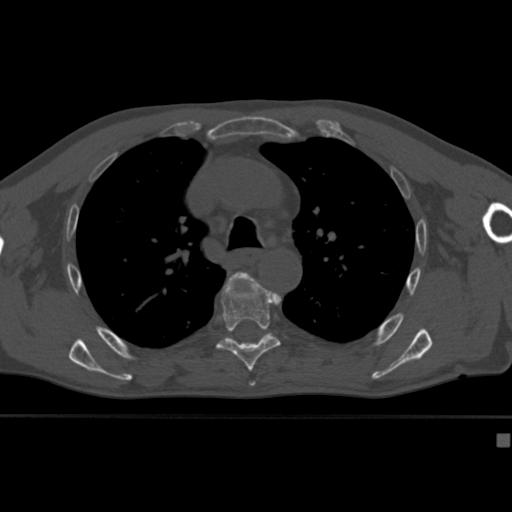
CT including the spine, one axial slice. Slice 295 of 430 in the series (ordered by position). Reconstruction kernel Br40s. Bone window (W 1800 / L 400 HU). 1.5 mm slice thickness. 512 × 512 image matrix. Patient: male, 64 years. From the clinical record (not read from this slice): primary cancer: uterus; vertebrae with lytic lesions (as recorded): T1, T4, T5, T7, L5.
Annotated regions visible in this slice (semi-automatically segmented with operator editing):
- T5 vertebra: bounding box [x1, y1, x2, y2] px = [230, 271, 255, 382]
- T6 vertebra: [216, 278, 281, 372]